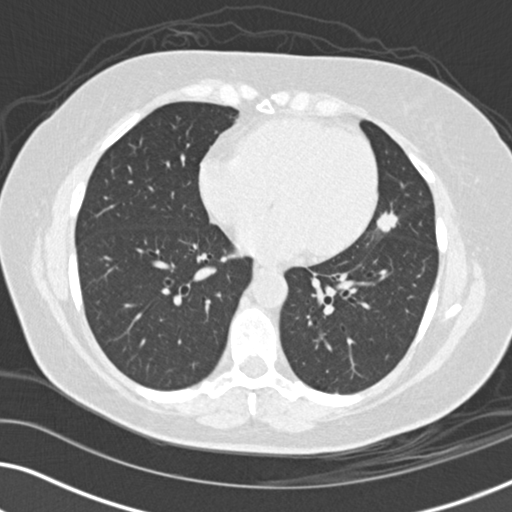
Low-dose screening chest CT, one axial slice; position 68 of 152 along the scan axis; reconstruction kernel B30f; 120 kVp; lung window (W 1500 / L -600 HU); 512 × 512 image matrix, field of view 330 × 330 mm.
Structures marked on this image (manually delineated by an expert):
- lesion 1 (tumor, upper lobe of left lung): bounding box (x1, y1, x2, y2) in pixels: (377, 212, 398, 232)